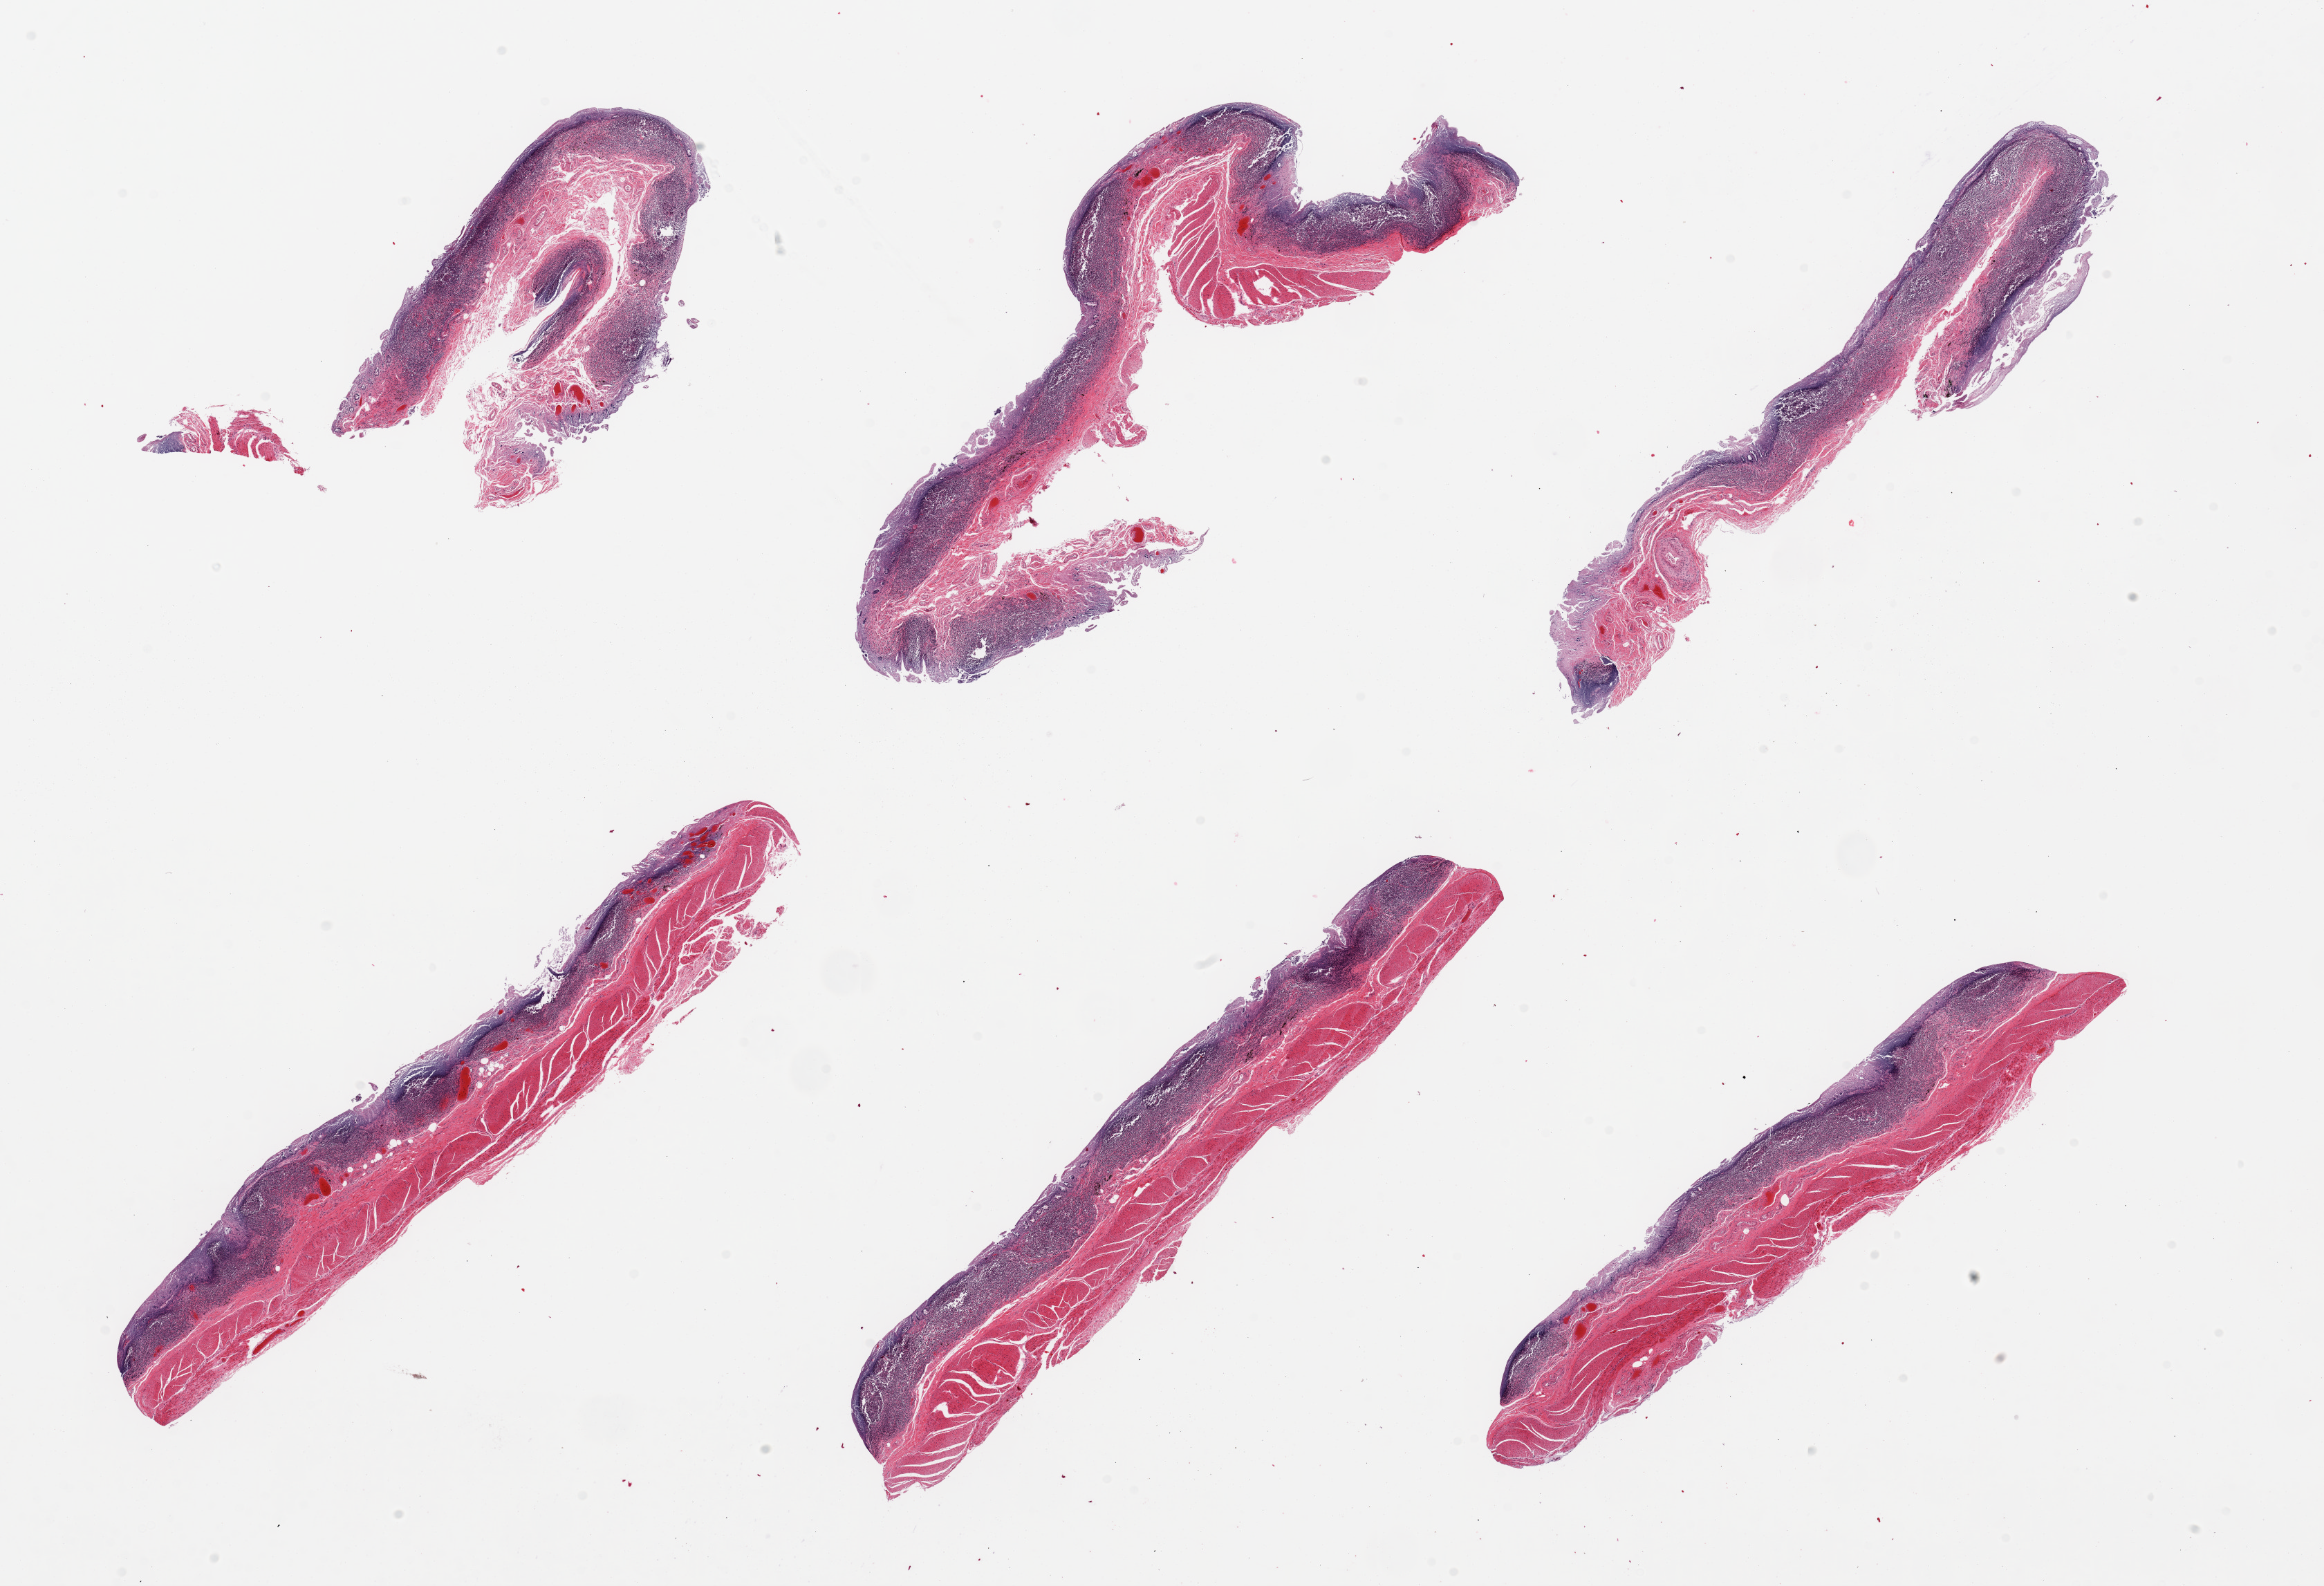
Whole-slide image, H&E stain — low-resolution overview of the scanned area, about 26.6 x 18.1 mm (from a 20x scan), PAXgene-fixed, paraffin-embedded tissue, target tissue: ileum, tissue donor sample. Donor sex: male.
* review note (as recorded): 6 pieces; severely autolyzed mucosa, but residual lymphoid component, muscularis also present (not target)